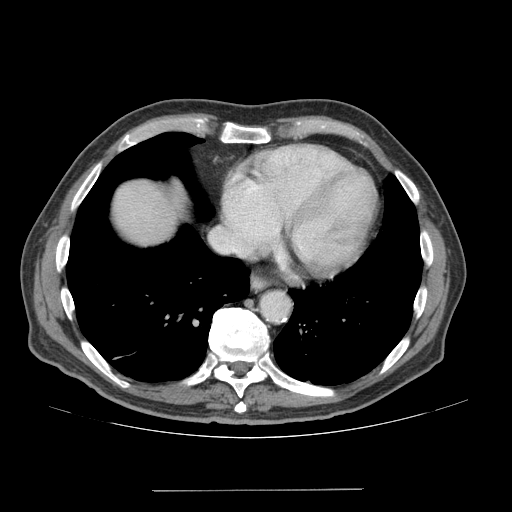
Contrast-enhanced abdominal CT (liver protocol), one axial slice. Reconstruction kernel STANDARD. Soft-tissue window (W 400 / L 40 HU). 2.5 mm slice thickness. 512 × 512 image matrix, field of view 400 × 400 mm. From the clinical record (not read from this slice): diagnosis: hepatocellular carcinoma (patient treated with transarterial chemoembolisation; whether this scan precedes or follows treatment is not stated here); TNM stage (as recorded): Stage-IVA; Child-Pugh class: A; tumour differentiation: well differentiated; tumour nodularity: uninodular.
Annotated regions visible in this slice (semi-automatic segmentation, software-assisted and operator-edited):
- liver parenchyma outside the tumour (the mass and vessels are separate outlines, so this box may not span the whole liver): bounding box (x1, y1, x2, y2) in pixels: (114, 180, 184, 244)